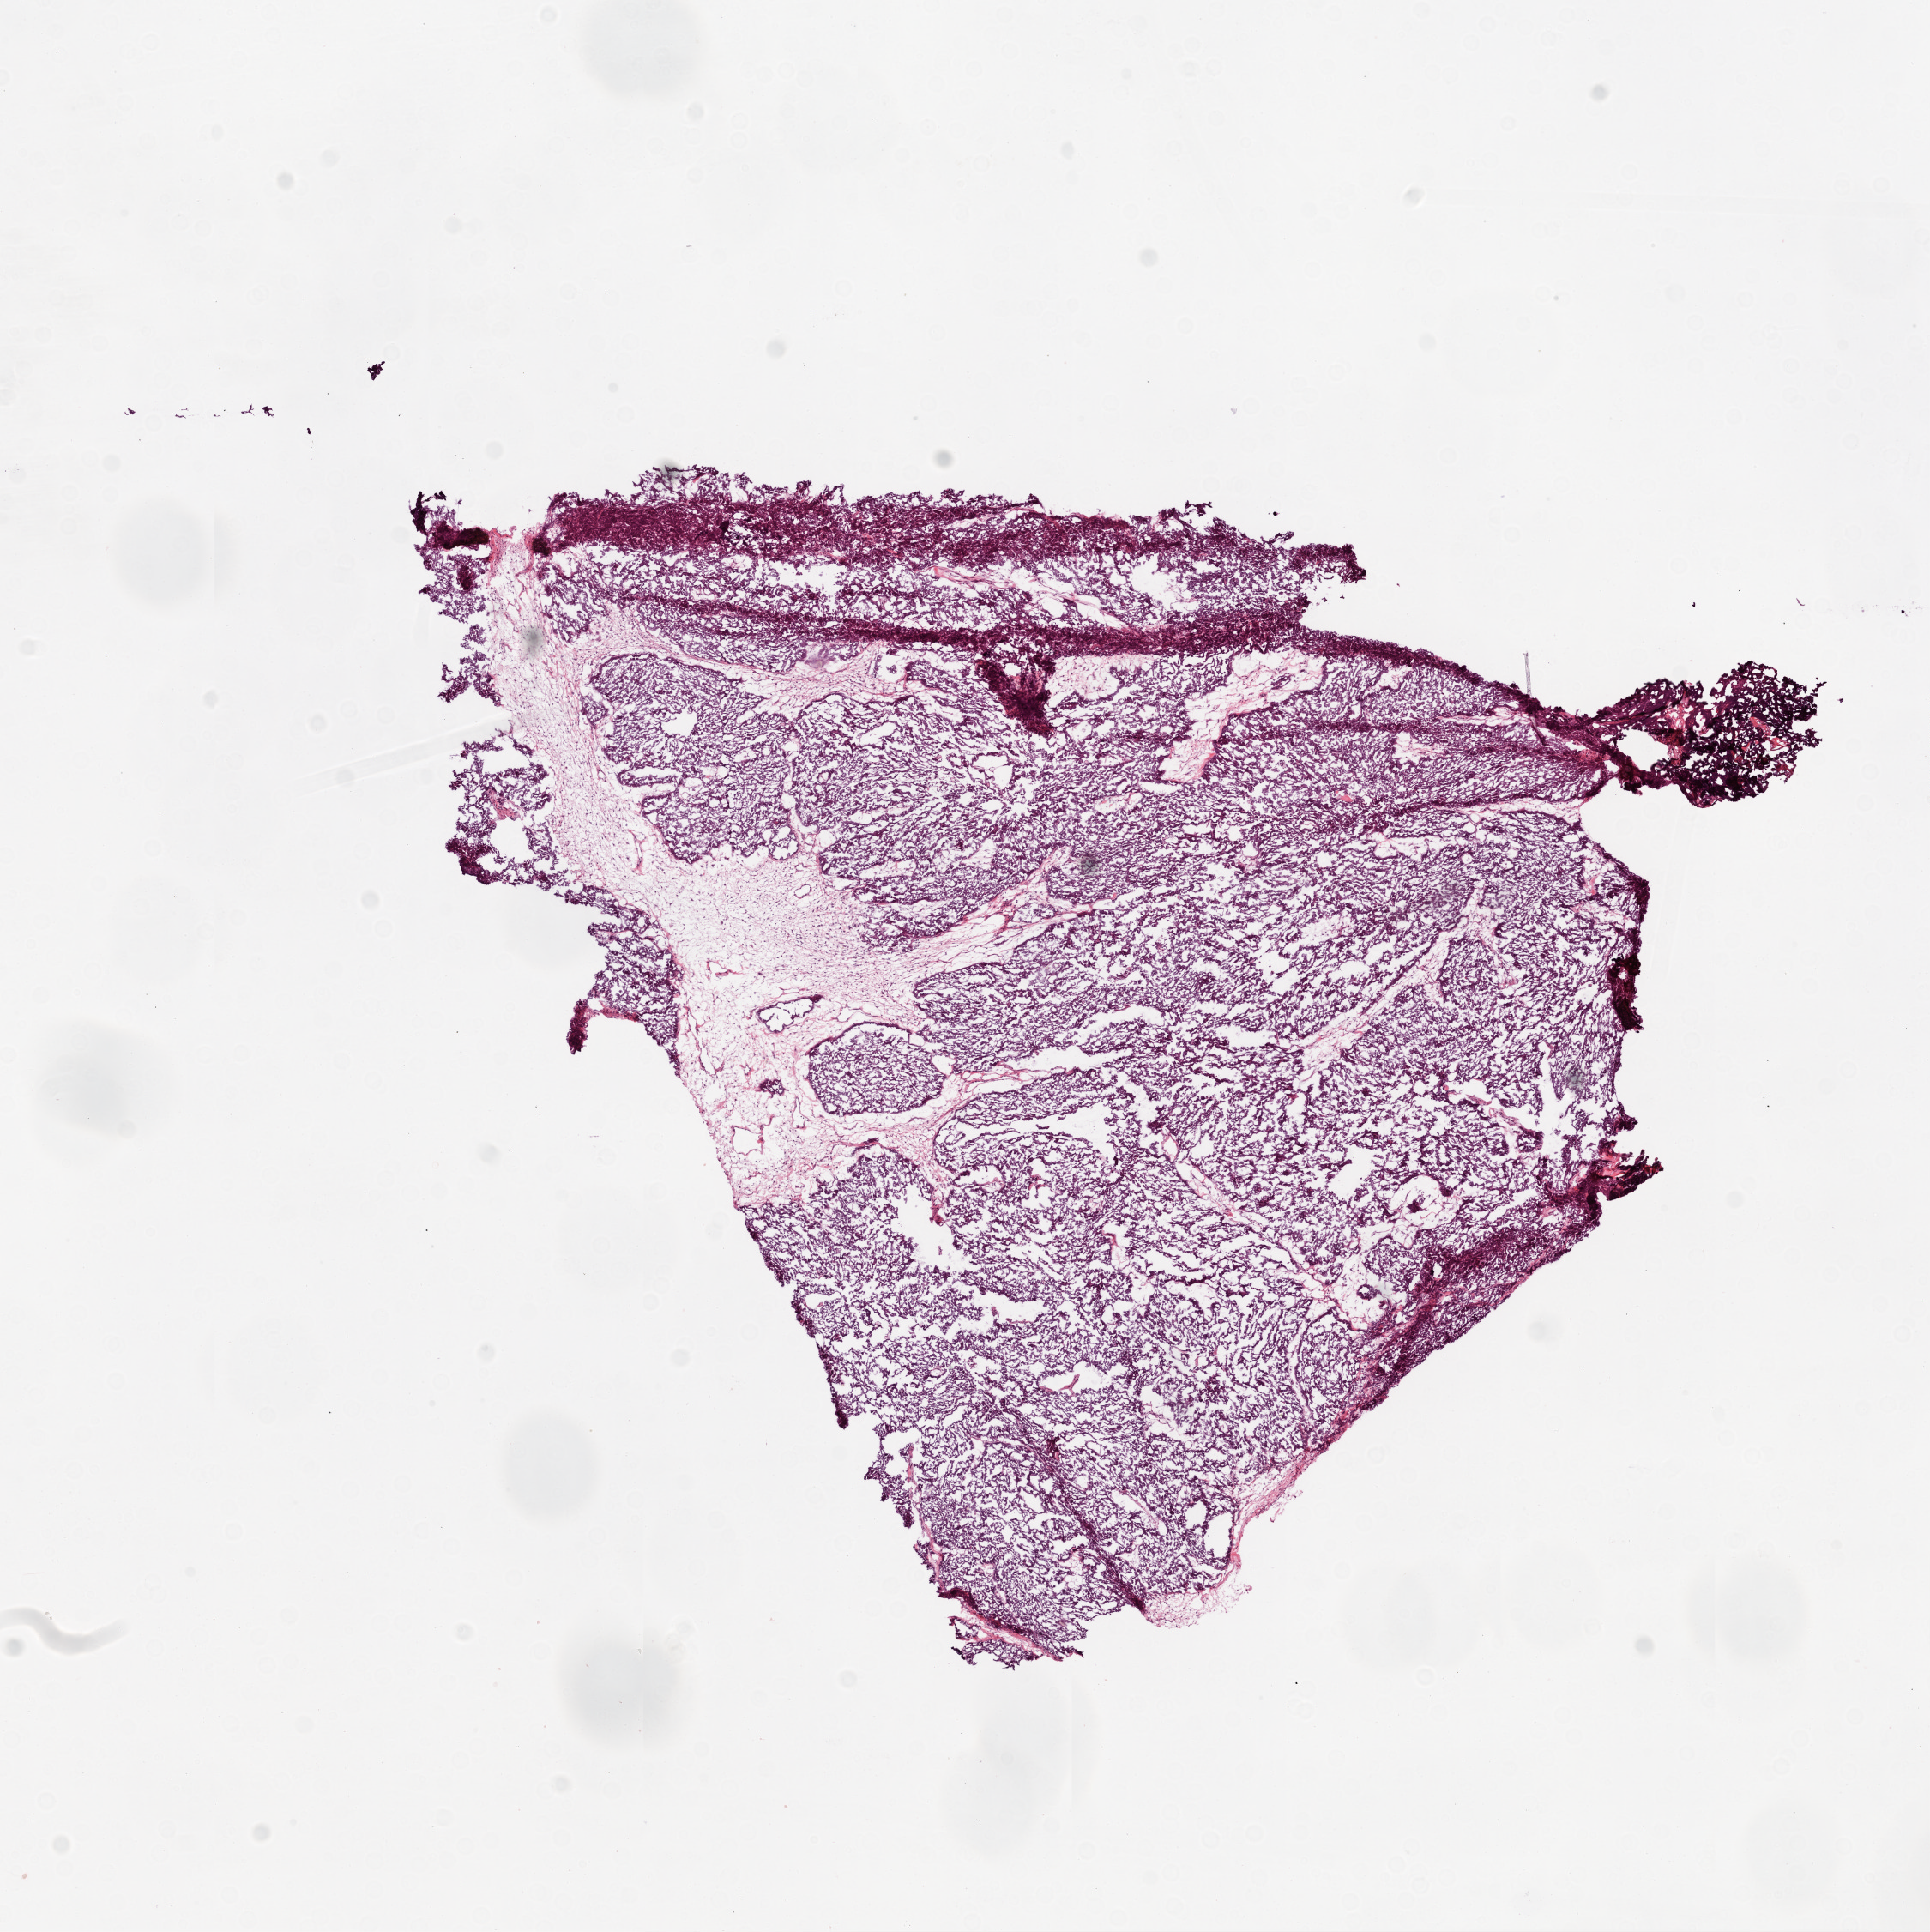
Whole-slide histology image, Hematoxylin and eosin (H&E) stained — low-resolution overview of the scanned area, about 9.0 x 9.0 mm (from a 20x scan). Frozen section from the top of the tissue portion. Sample: primary tumour, ovary. Patient: female, age at initial diagnosis 73 years. Histologic grade: G2 (moderately differentiated). Slide review estimates, as recorded: tumour cells 100%, tumour nuclei 85%, normal cells 0%, stromal cells 0%, necrosis 0%. Infiltration values recorded for this section: lymphocyte infiltration 0%, monocyte infiltration 0%, neutrophil infiltration 0%.
FIGO stage: IIIC. Pathologic diagnosis: Serous cystadenocarcinoma, NOS.